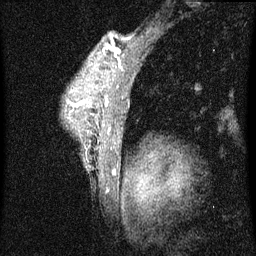
Breast MRI (dynamic contrast-enhanced), one sagittal slice. Position 55 of 60 along the scan axis. Dynamic contrast-enhanced series, image 2 of 4 at this slice position (ordered by acquisition). 1.5 T. TE 4.2 ms, TR 8 ms. 2 mm slice thickness. 256 × 256 image matrix, field of view 180 × 180 mm. Patient: female, 50 years.
Outlined on this slice (semi-automatically segmented with operator editing):
- analysis volume of interest (the breast-tissue region the enhancement analysis was run in; not a lesion): bounding box [x1, y1, x2, y2] px = [67, 50, 124, 175]
- tumour enhancement mask (voxels above the 70 % enhancement threshold inside the analysis volume of interest): [107, 98, 109, 105]